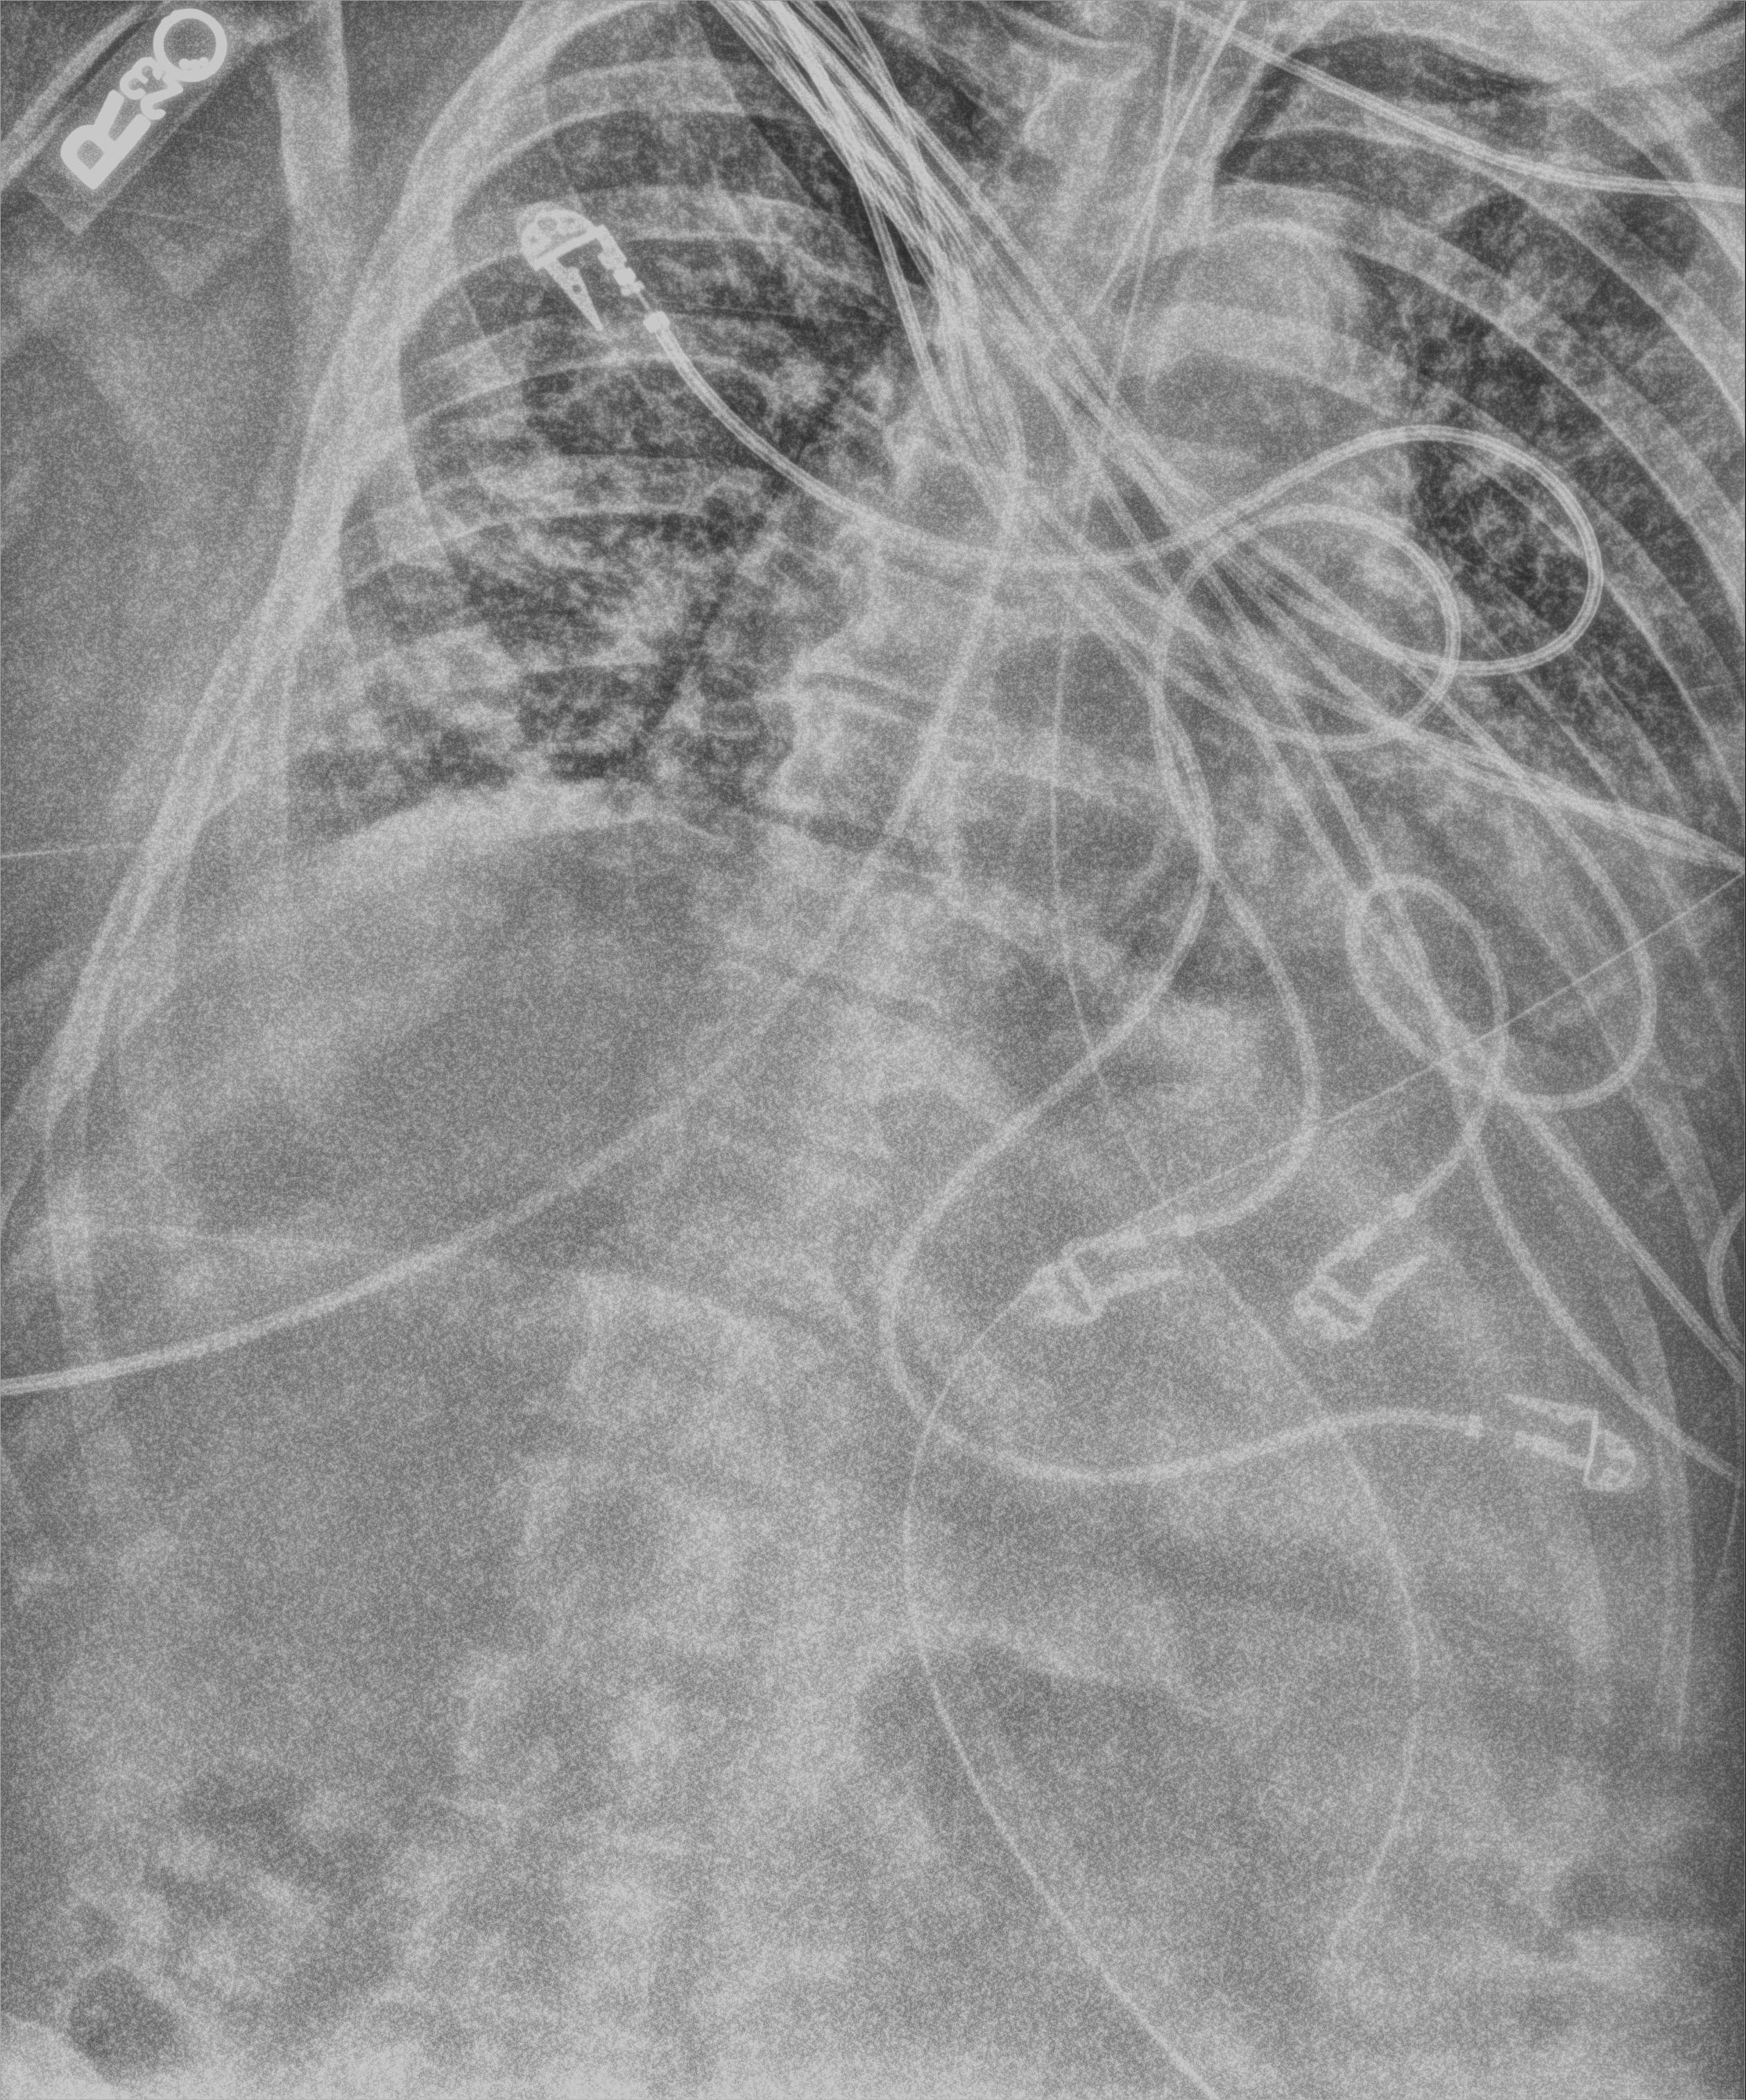
Chest X-ray (portable), anteroposterior (AP) projection. Patient hospitalised with COVID-19; male, aged 60–74 years.
From the hospital-stay record, not from the radiograph (when in the stay this image was taken is not recorded): hypertension (admission record): yes.